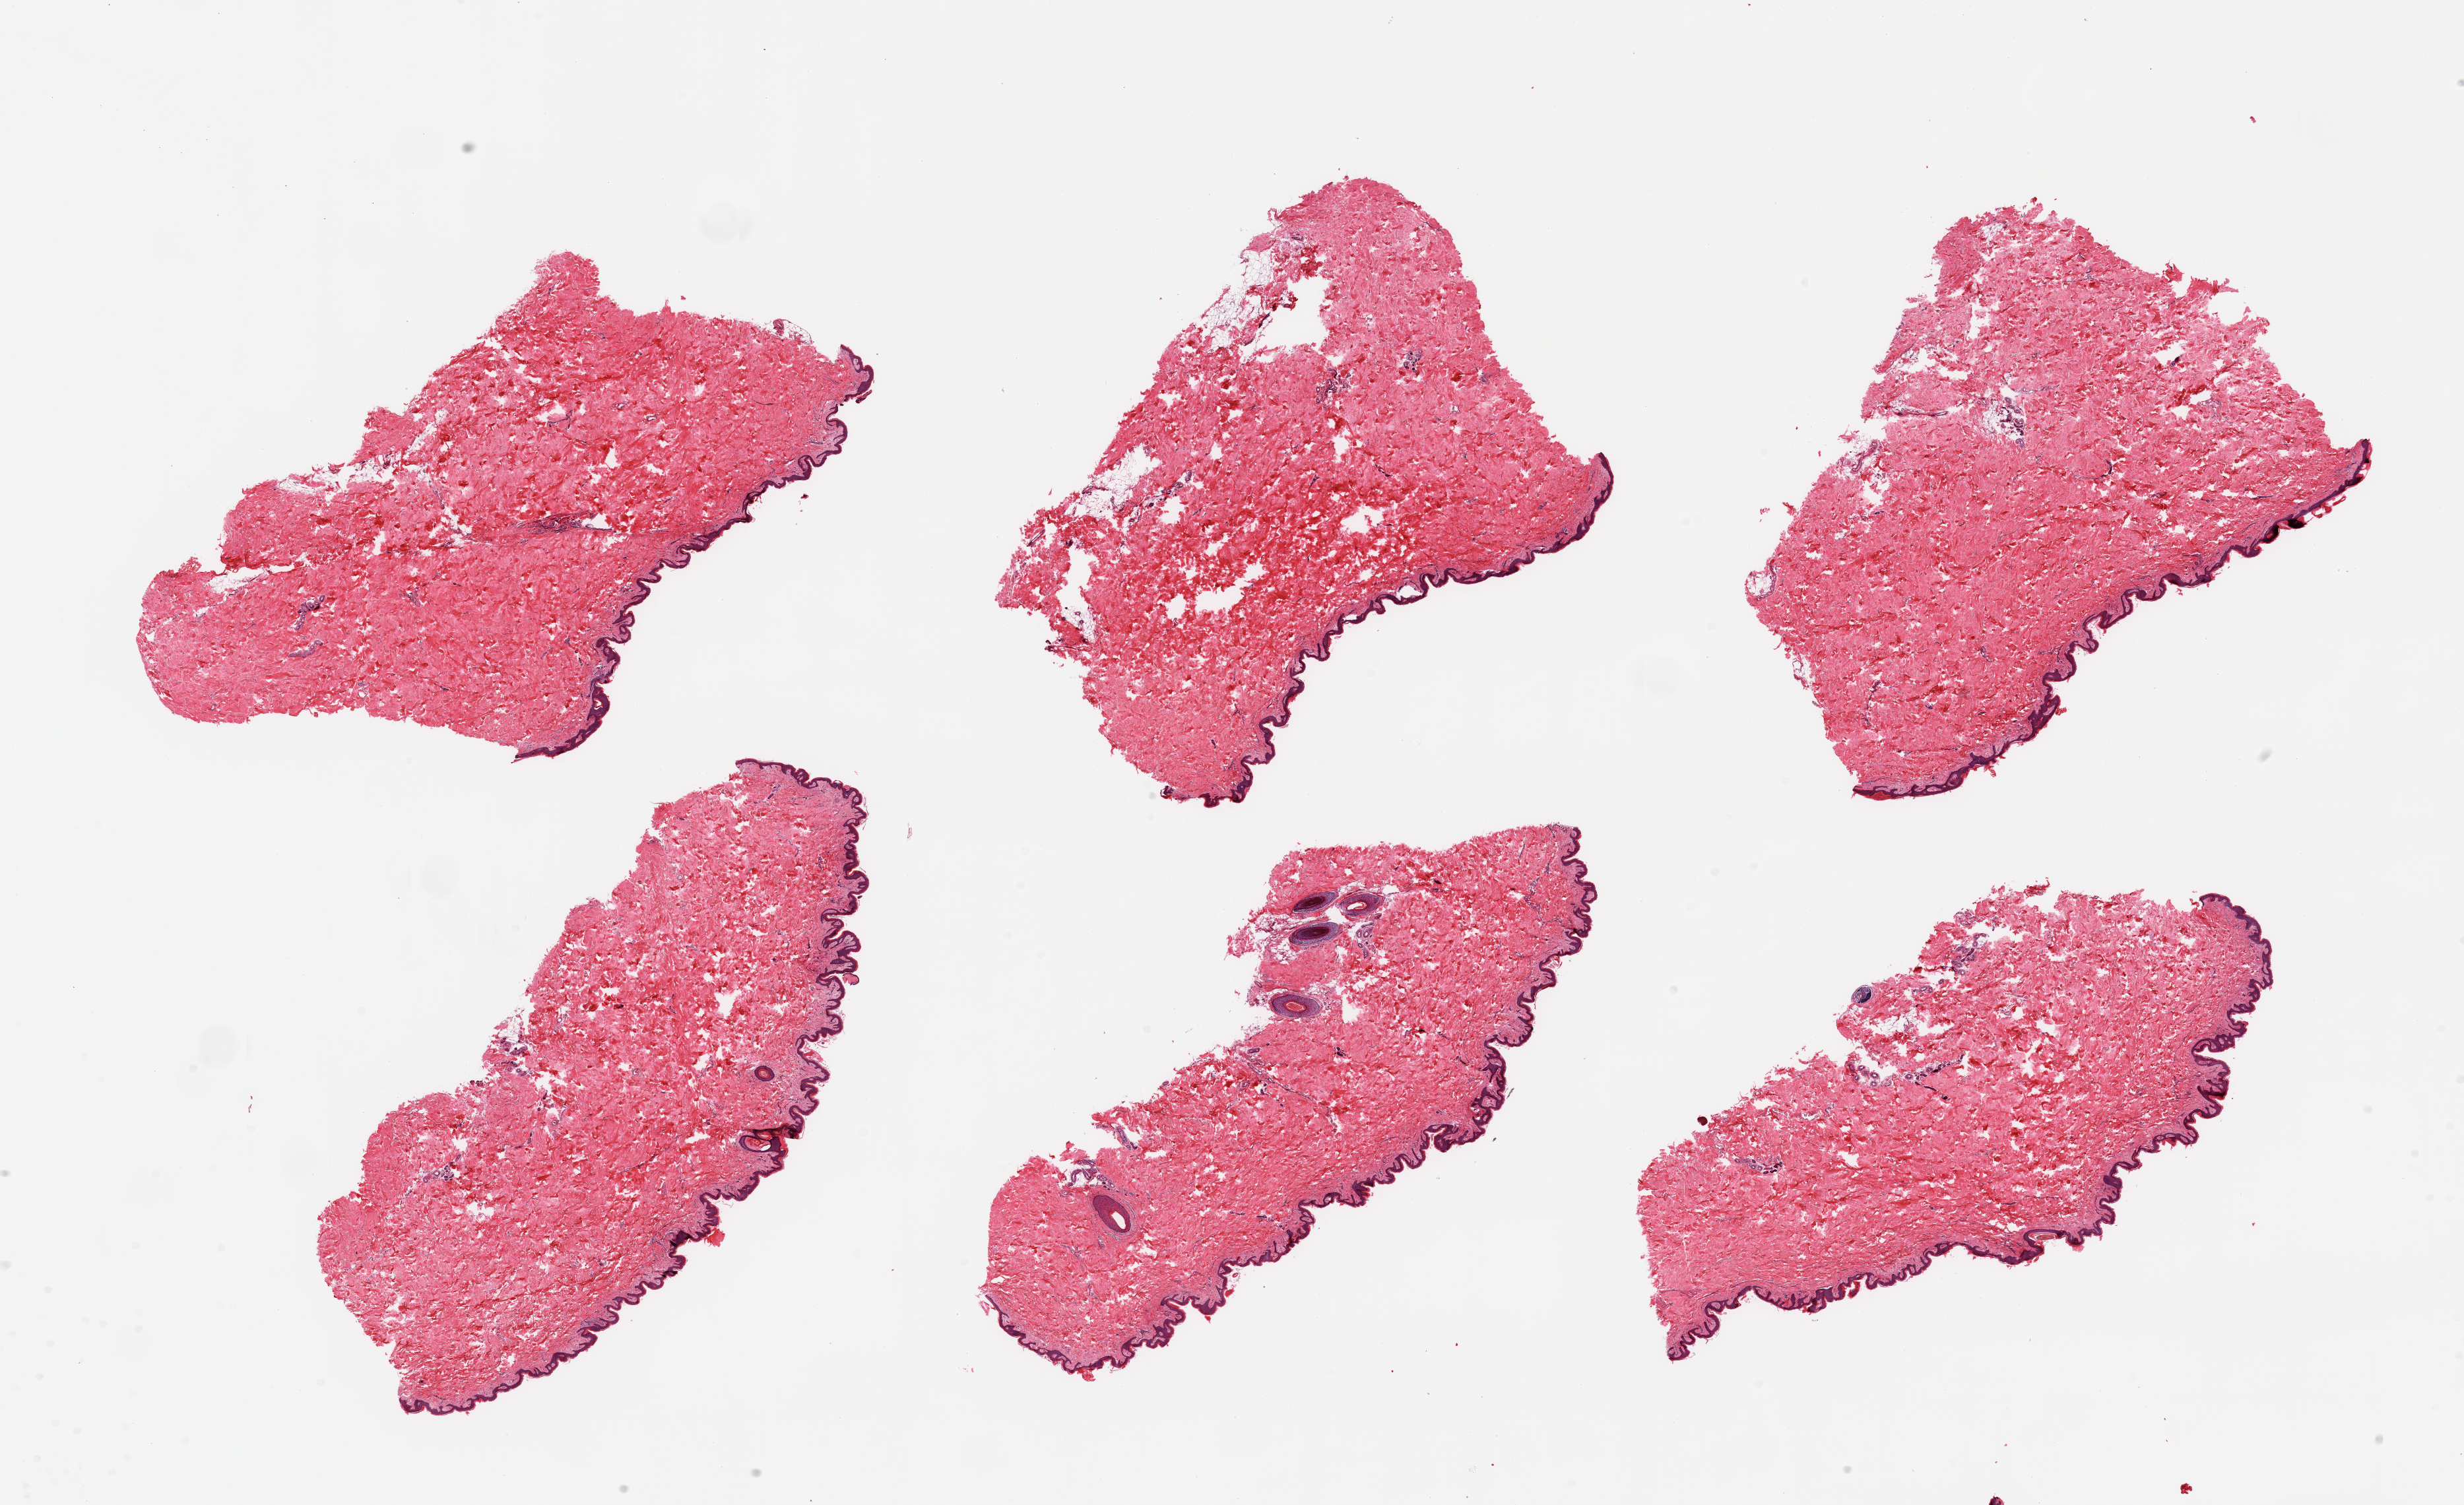
H&E whole-slide image, whole scanned area (about 29.5 x 18.0 mm, from a 20x scan) shown as a low-resolution overview; PAXgene-fixed, paraffin-embedded tissue; target tissue: skin of suprapubic region; donor tissue sample.
- review note (as recorded): 6 pieces, no dermal fat; squamous epithelium is ~30-40microns